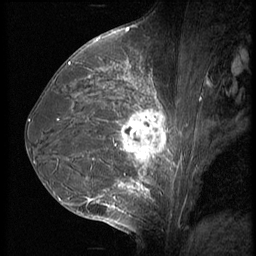
Breast MRI (dynamic contrast-enhanced), one sagittal slice; slice 31 of 56 in the series (ordered by position); 3 images stored at this slice position (order not interpretable as contrast timing); 1.5 T; TE 4.2 ms, TR 9 ms; 2.5 mm slice thickness; 256 × 256 image matrix. Patient: female, 35 years. From the clinical record (not read from this slice): setting: breast cancer imaged before/during neoadjuvant chemotherapy; receptor status: HR-positive, HER2-negative.
Structures marked on this image (semi-automatic segmentation, software-assisted and operator-edited):
- analysis volume of interest (the breast-tissue region the enhancement analysis was run in; not a lesion): bounding box <63,60,190,218> (left, top, right, bottom; pixels)
- tumour enhancement mask (voxels above the 140 % enhancement threshold inside the analysis volume of interest): <69,63,167,199>